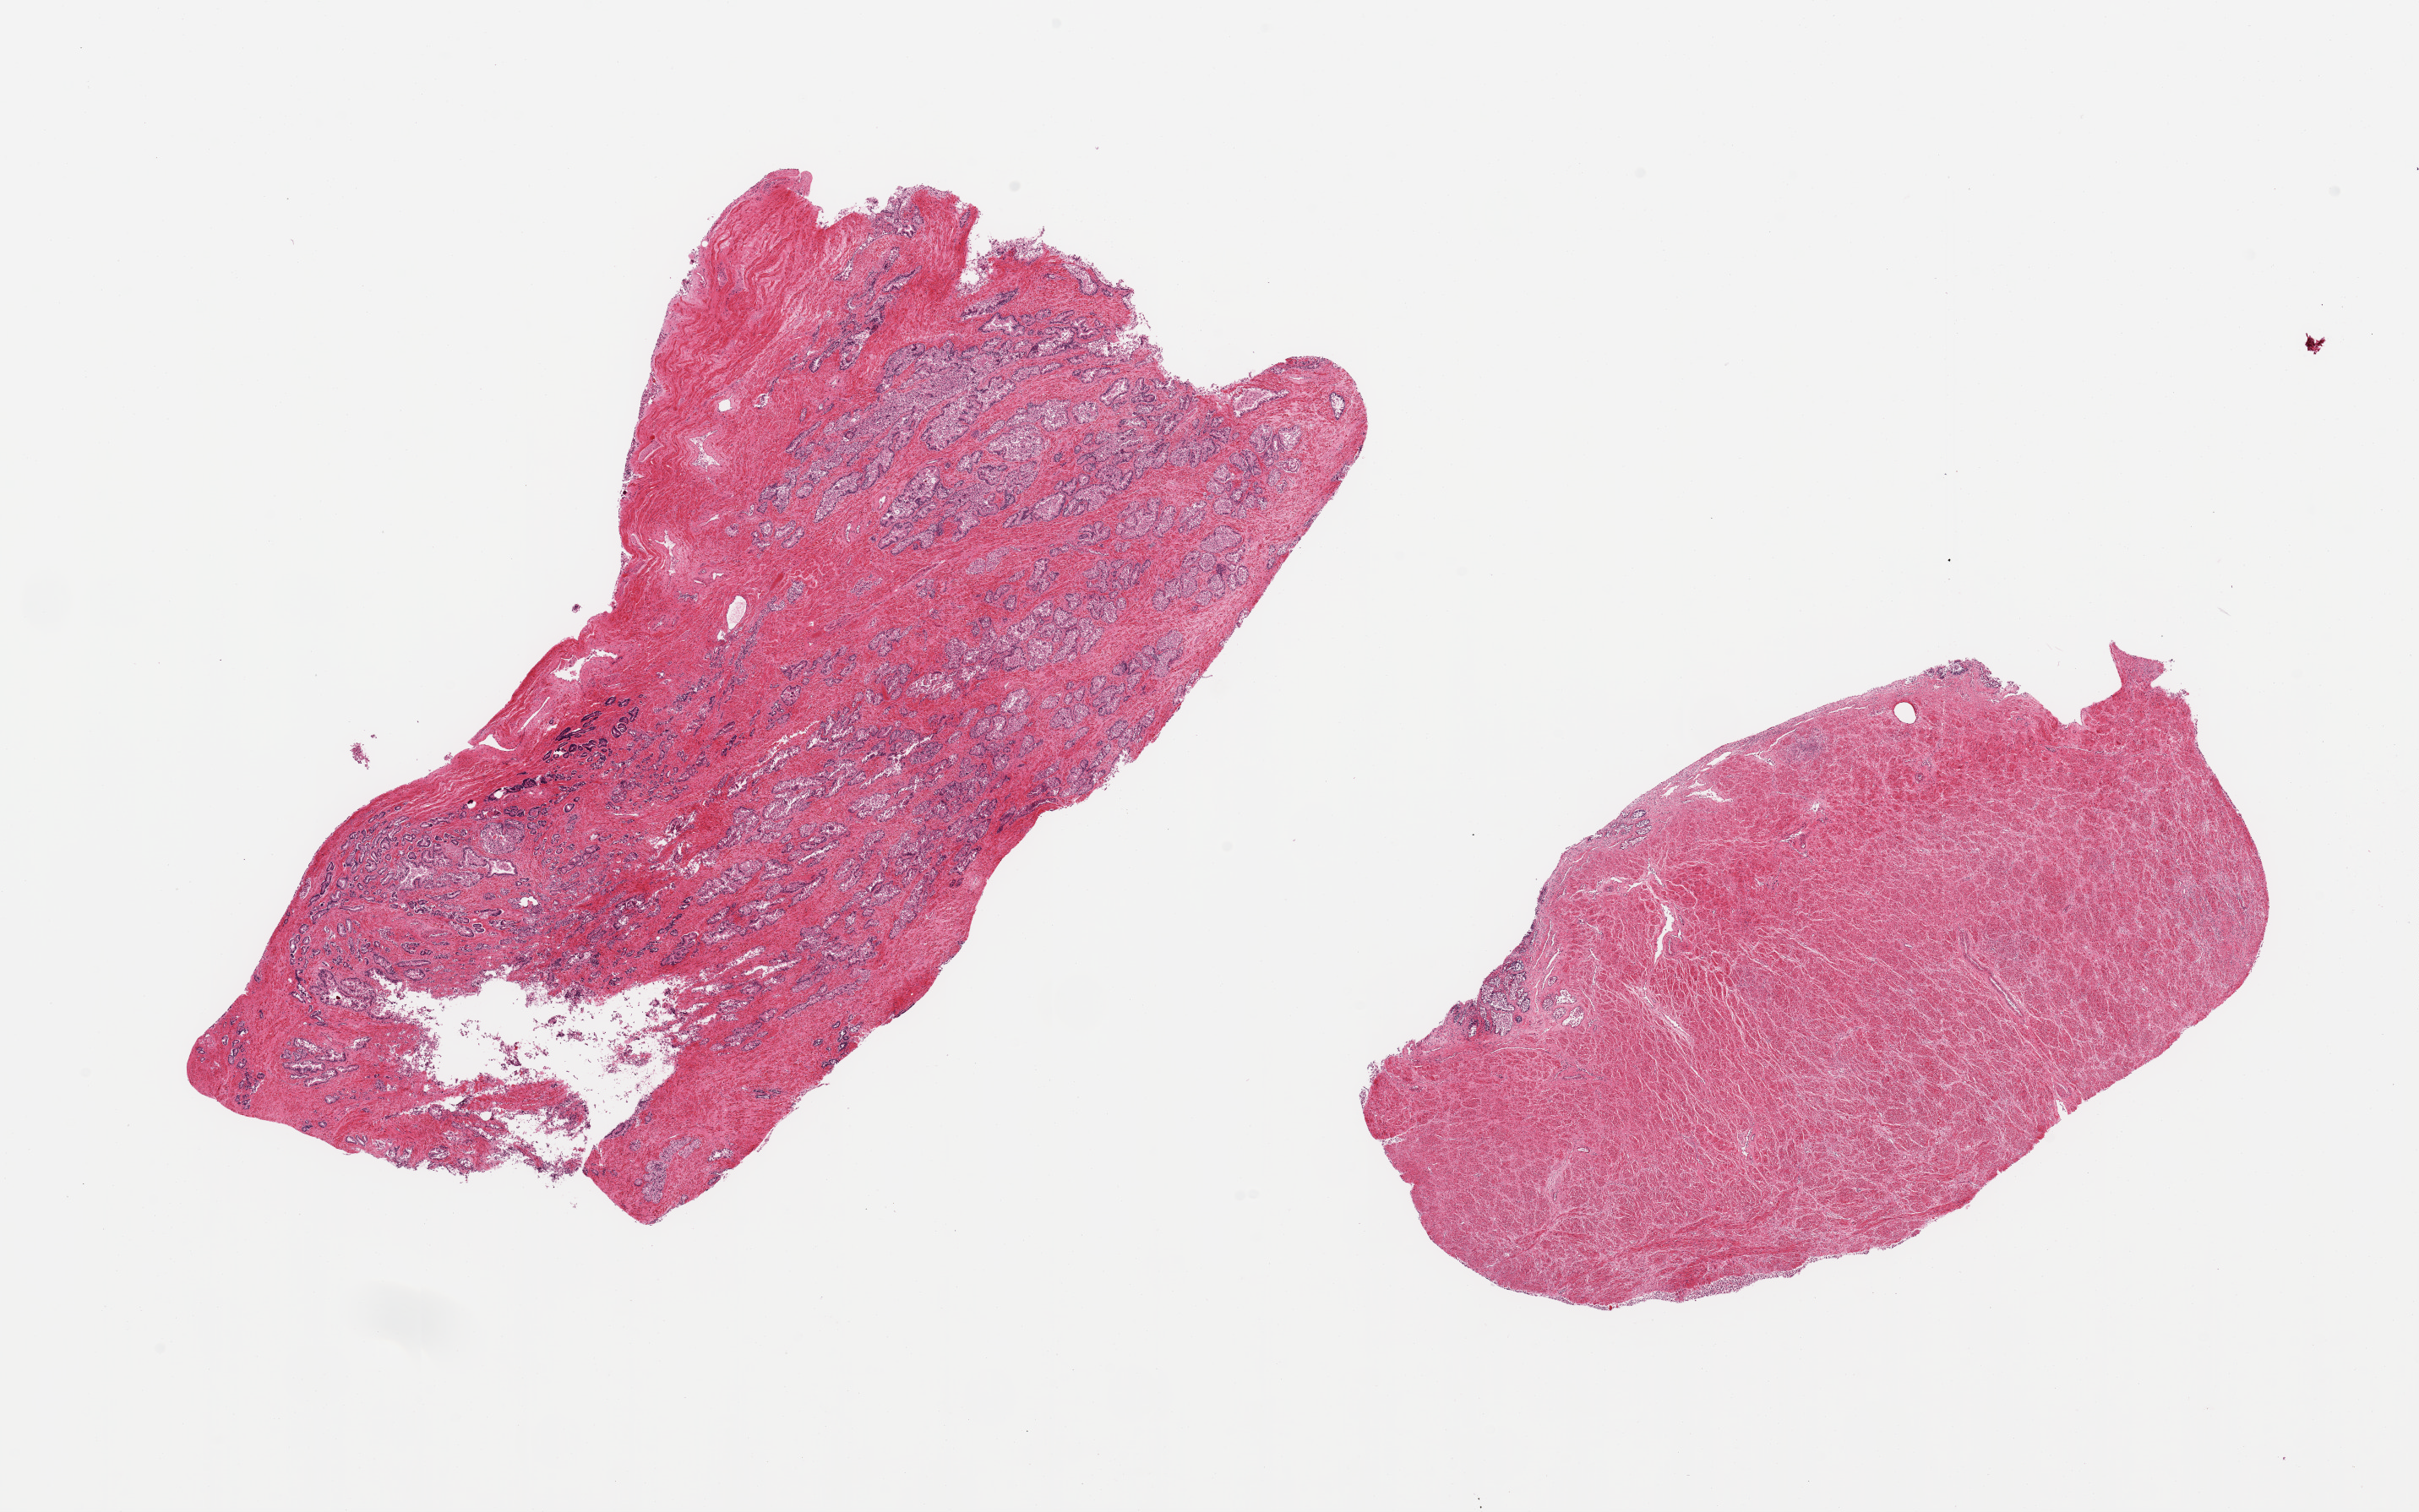
Haematoxylin and eosin whole-slide image — a low-resolution overview of the entire scanned area, about 22.6 x 14.2 mm, PAXgene-fixed paraffin-embedded (PFPE) section, sampled site (target tissue): prostate, donor tissue sample. Male donor.
Pathologist's review note for this sample: 2 pieces, glandular elements with advanced autolysis, hyperplastic pattern.